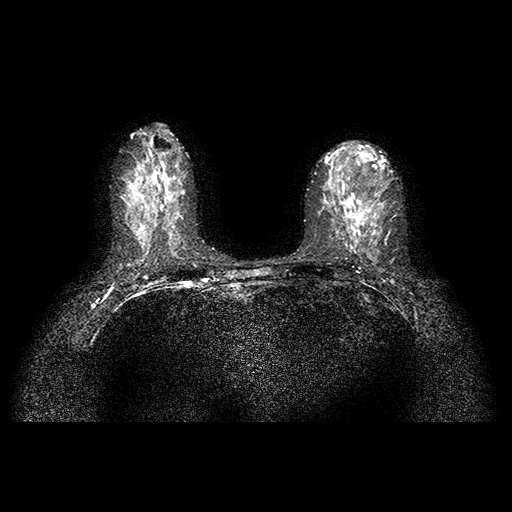
Breast MRI examination; 2 images, each one mid-volume slice chosen by position. Patient in her 40s.
Image 1: axial T2-weighted / STIR image, slice 45 of 88, 2 mm slice thickness.
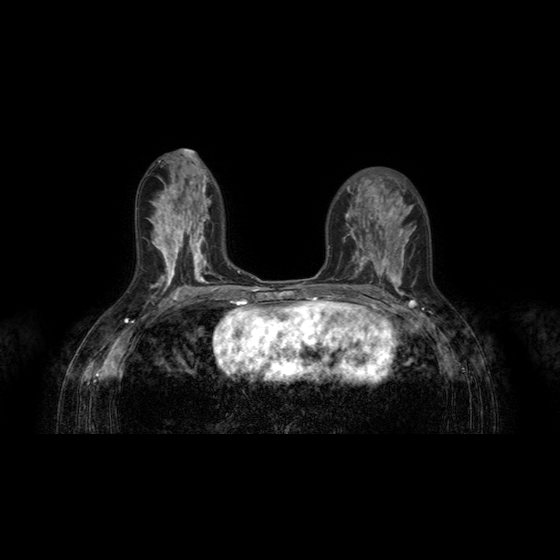
Image 2: post-contrast dynamic axial slice, slice 40 of 78, dynamic phase 5 of 8, 4 mm slice thickness.
Pathology recorded for this patient (not read from these images): pathology diagnosis: intraductal CA (left breast); receptor status (as recorded): ER neg, PR neg, HER2 pos; clinical background (as recorded): history of left breast cancer treated with lumpectomy and radiation therapy.